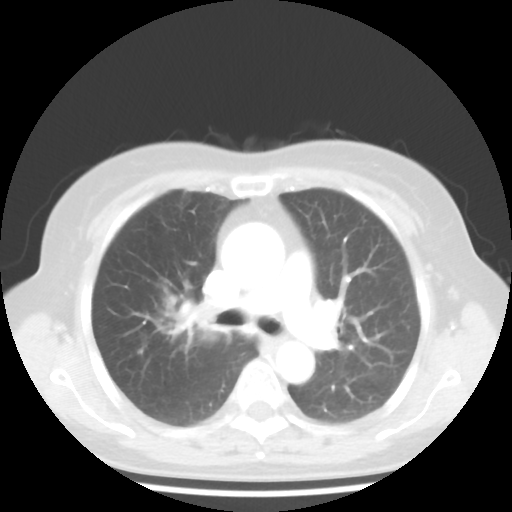
Chest CT, one axial slice. Slice 27 of 44 in the series (ordered by position). Reconstruction kernel STANDARD. 100 kVp. Lung window (W 1500 / L -600 HU). 5 mm slice thickness. 512 × 512 image matrix, field of view 316 × 316 mm. Female patient, age 62 years. Case-level facts recorded for this patient, not image findings: clinical TNM (as recorded): T3 N0 M0; histopathological grade: G3.
Outlined on this slice (bounding box drawn by a radiologist):
- lung tumour (recorded histology: small cell carcinoma): box from (x=158, y=295) to (x=222, y=345) px